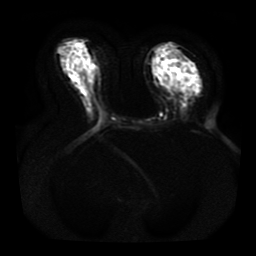
Breast MRI, one axial slice. Slice 21 of 41 in the series (ordered by position). Diffusion-weighted series; image 2 of 4 stored at this slice position (different b-values; order by instance number). 1.5 T. 5 mm slice thickness. 256 × 256 image matrix. Female patient.
Outlined on this slice (outlined manually by an expert reader):
- tumour on diffusion-weighted imaging: box from (x=182, y=78) to (x=186, y=82) px